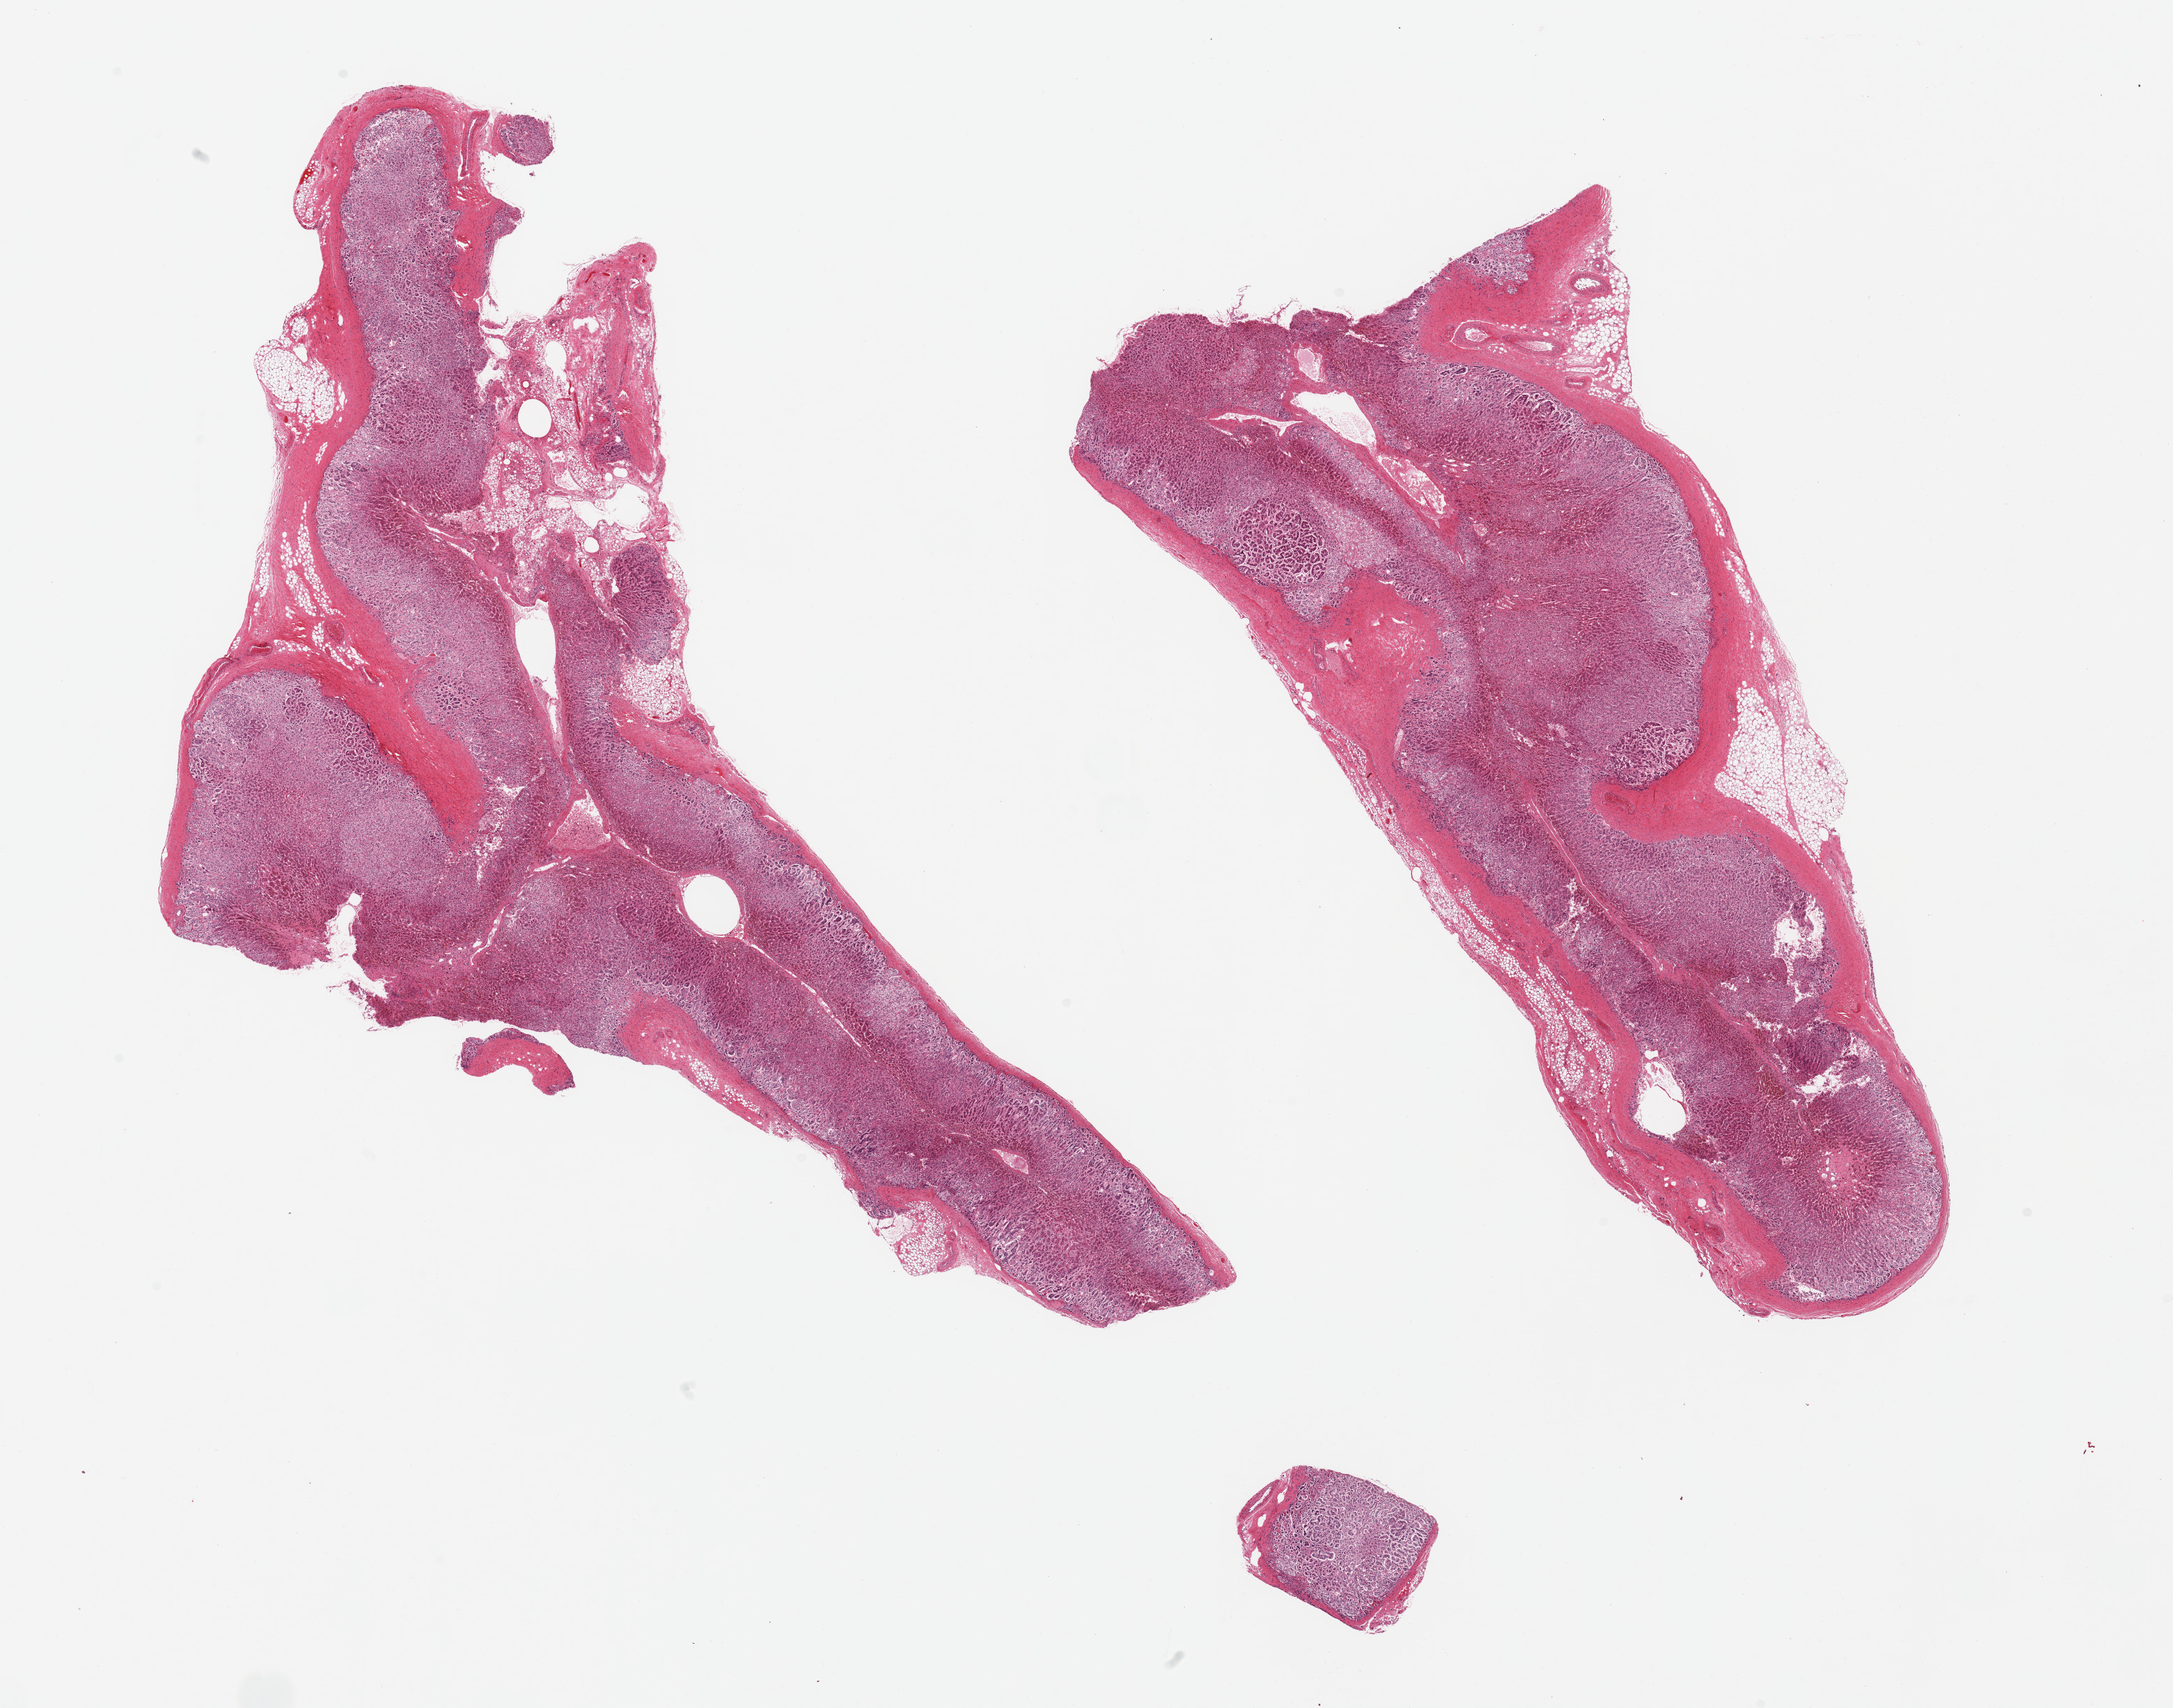
Digitized H&E-stained section, brightfield, low-resolution overview of the scanned area, about 24.6 x 19.3 mm (slide scanned at 20x), PAXgene-fixed paraffin-embedded (PFPE) section, target tissue: adrenal gland, tissue donor sample. Donor: male.
• reviewer comment on this tissue sample: 2 pieces; small amount of adherent fat